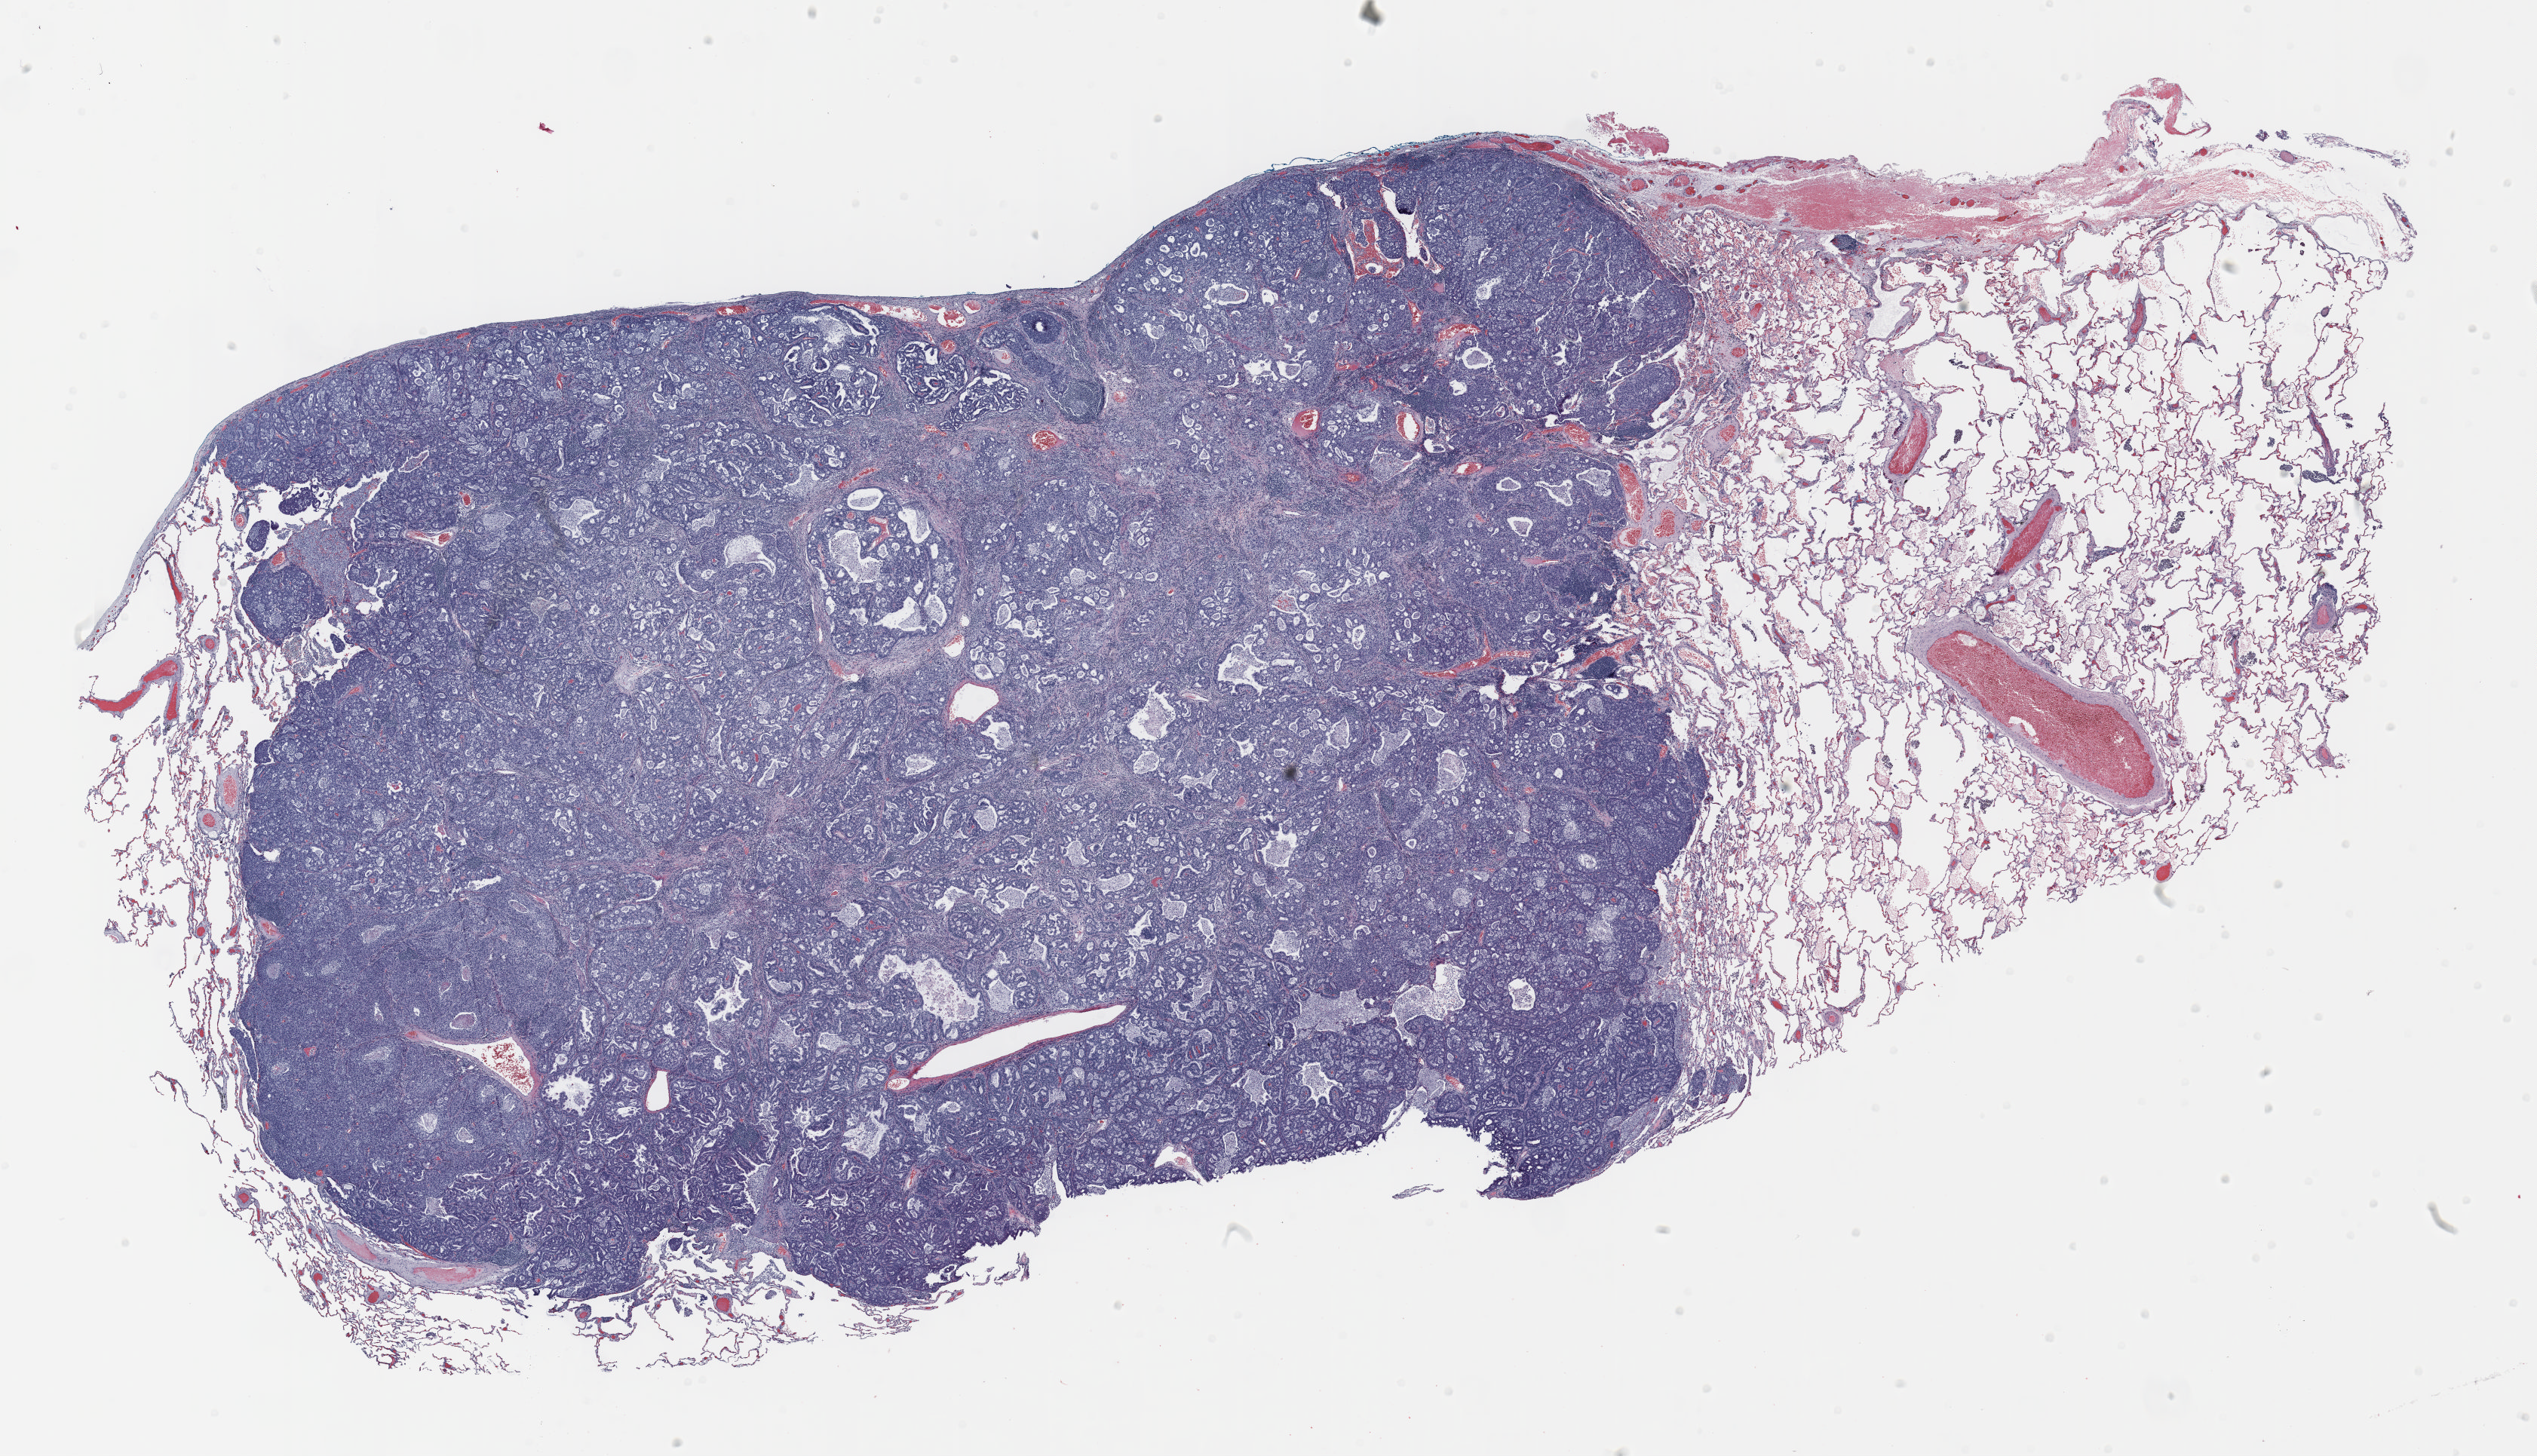
Whole-slide histology image, H&E, whole scanned area (about 27.0 x 15.5 mm) shown as a low-resolution overview, FFPE section, lung tissue. Male patient, aged 56 at enrolment. Grade: moderately differentiated (G2).
* participant's lung-cancer diagnosis: Adenocarcinoma, NOS
* stage (AJCC 6th edition): IA
* primary tumour location (clinical record): right middle lobe
* tumour size (pathology): 17 mm